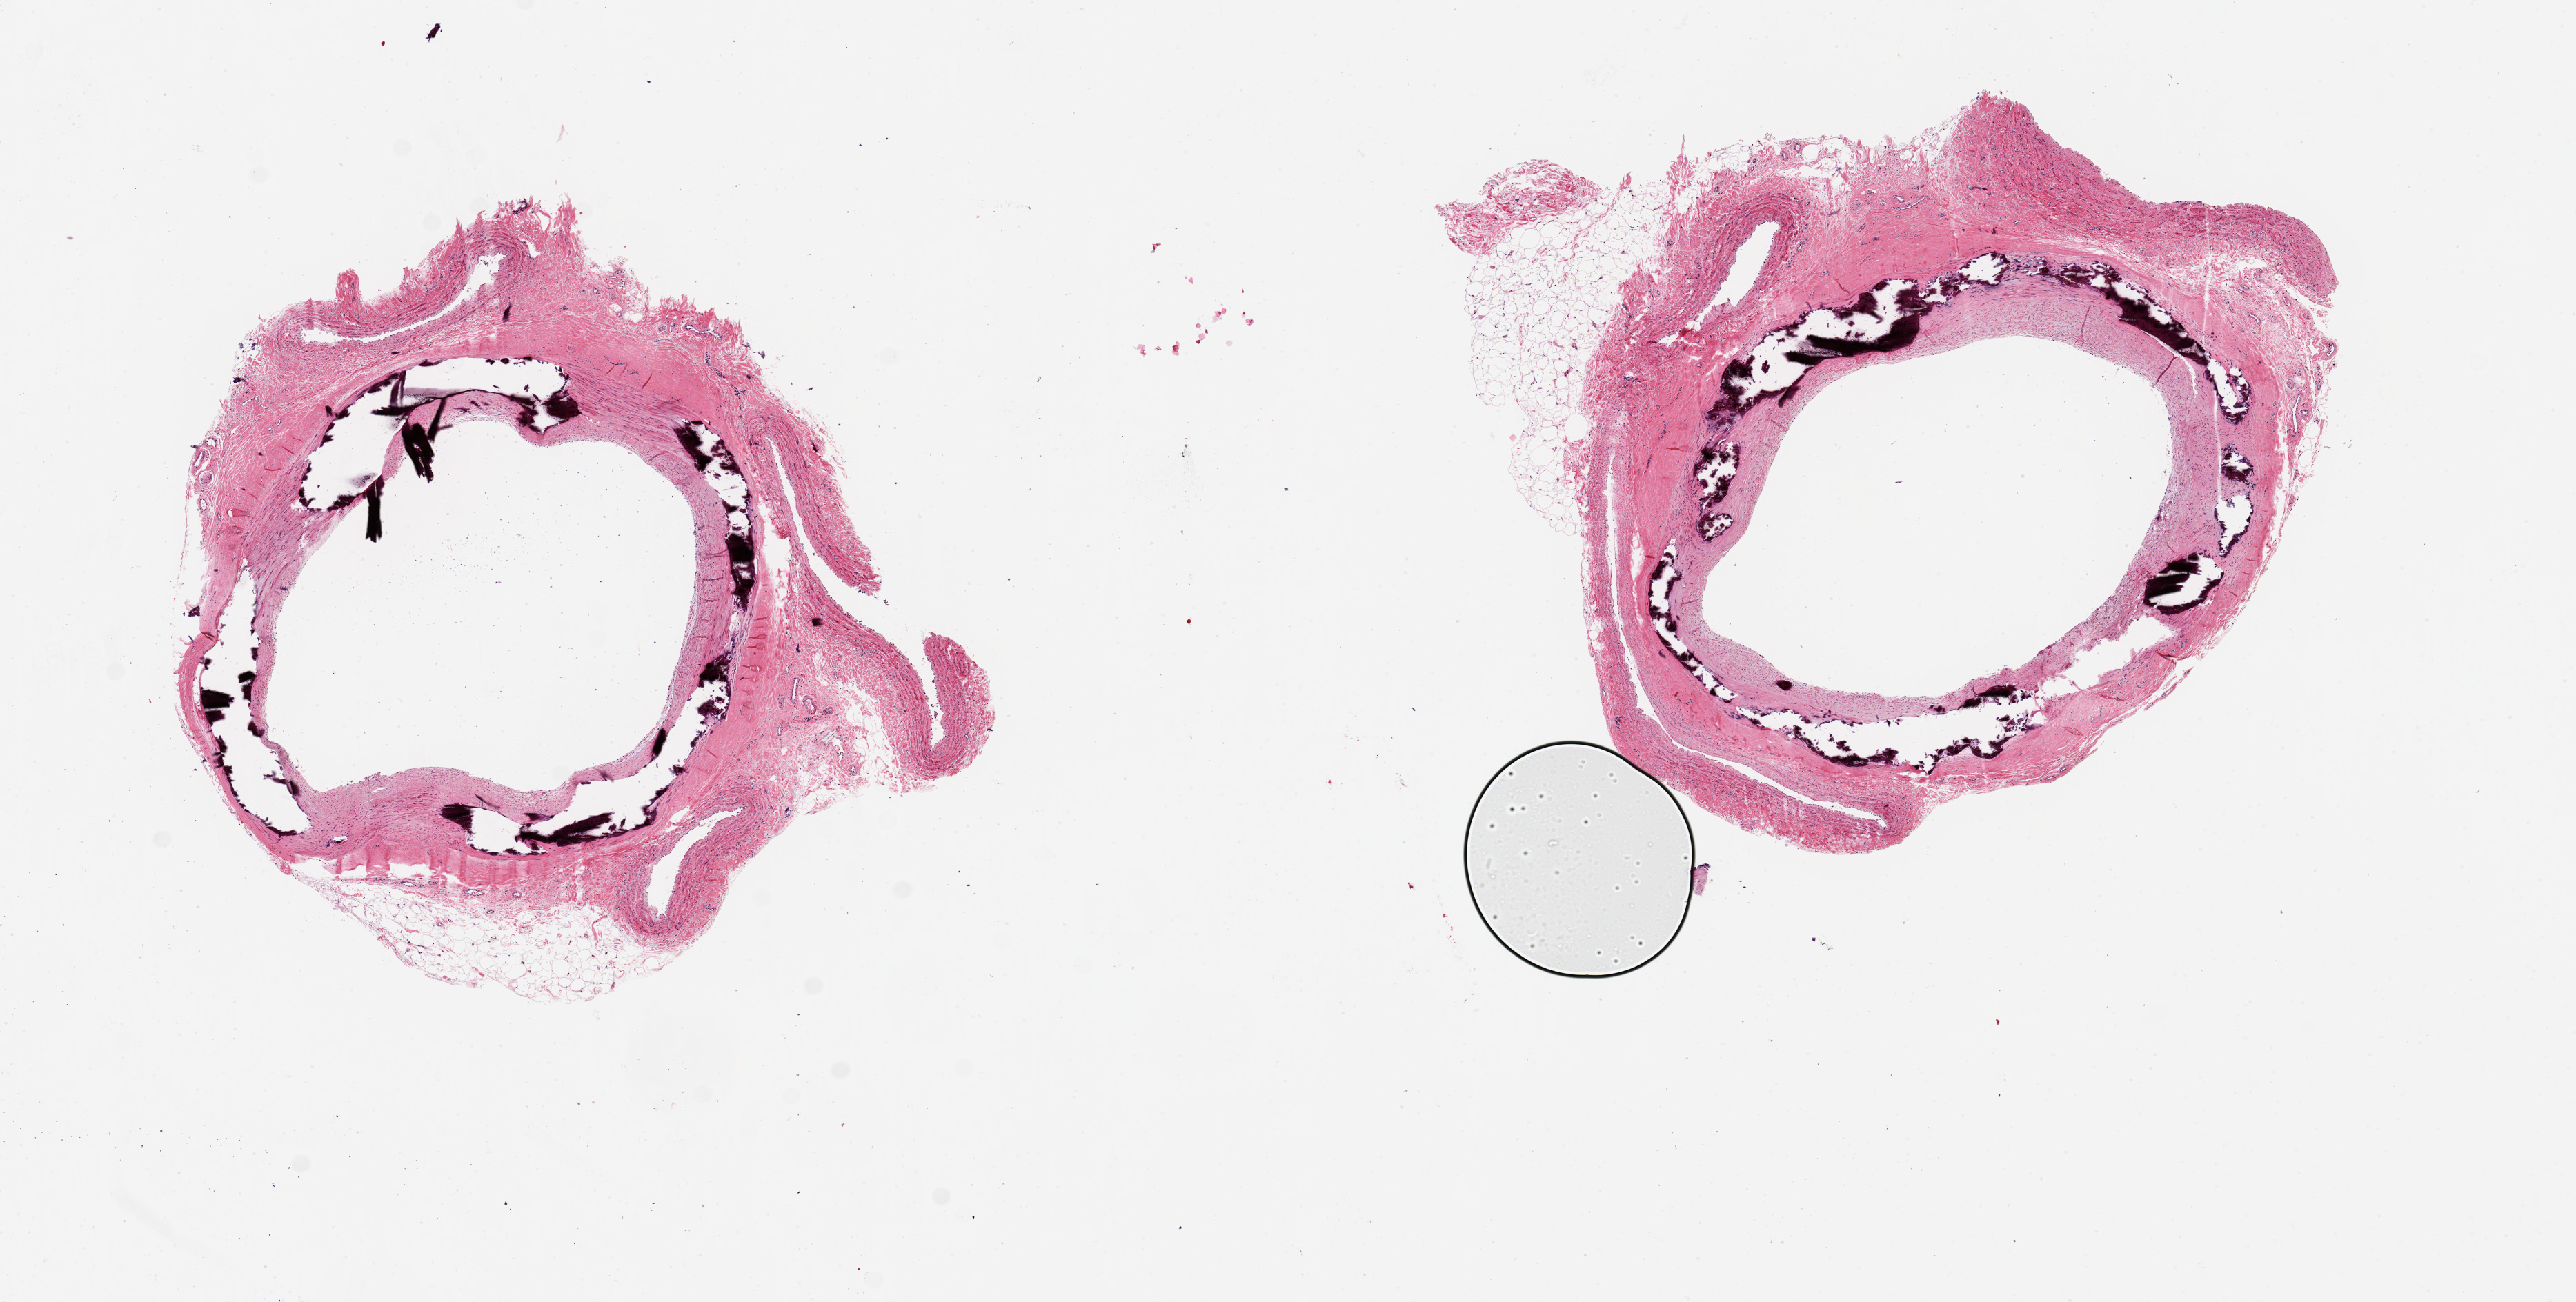
Digitized hematoxylin and eosin (H&E)-stained section — whole scanned area (about 14.8 x 7.5 mm, slide scanned at 20x) shown as a low-resolution overview. PAXgene-fixed, paraffin-embedded tissue. Target tissue: tibial artery. Tissue donor sample. Donor: male.
• reviewer comment on this tissue sample: 2 pieces, ~4mm d. Extensive Monckeberg???s medial sclerosis in both aliquots